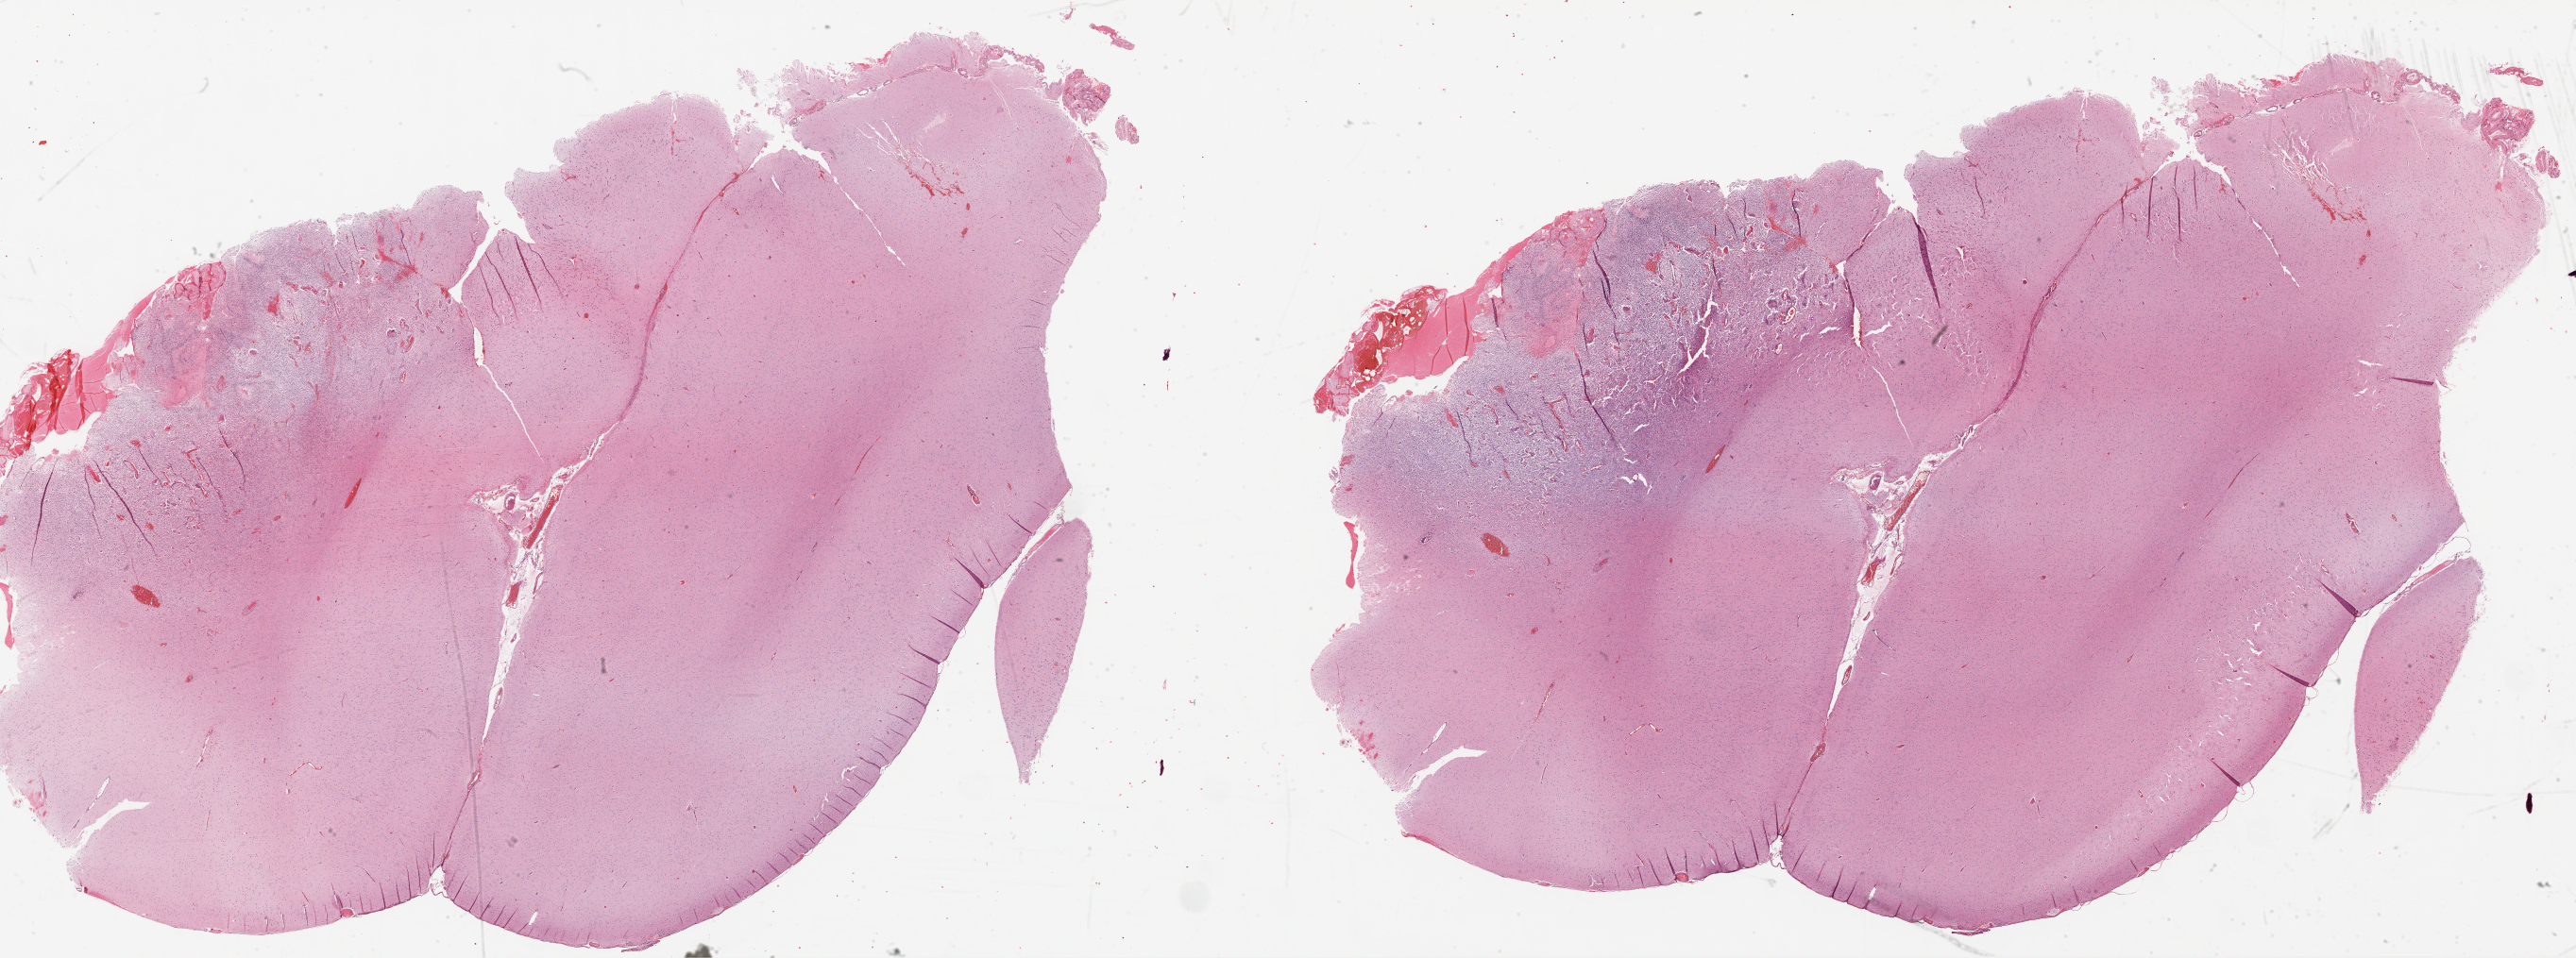
Whole-slide histology image, Hematoxylin and eosin (H&E) stained — low-resolution overview of the scanned area, about 44.0 x 16.4 mm, formalin-fixed paraffin-embedded (FFPE) diagnostic section, brain, primary tumour sample. Male patient; age at initial diagnosis 54 years.
* pathologic diagnosis: Glioblastoma